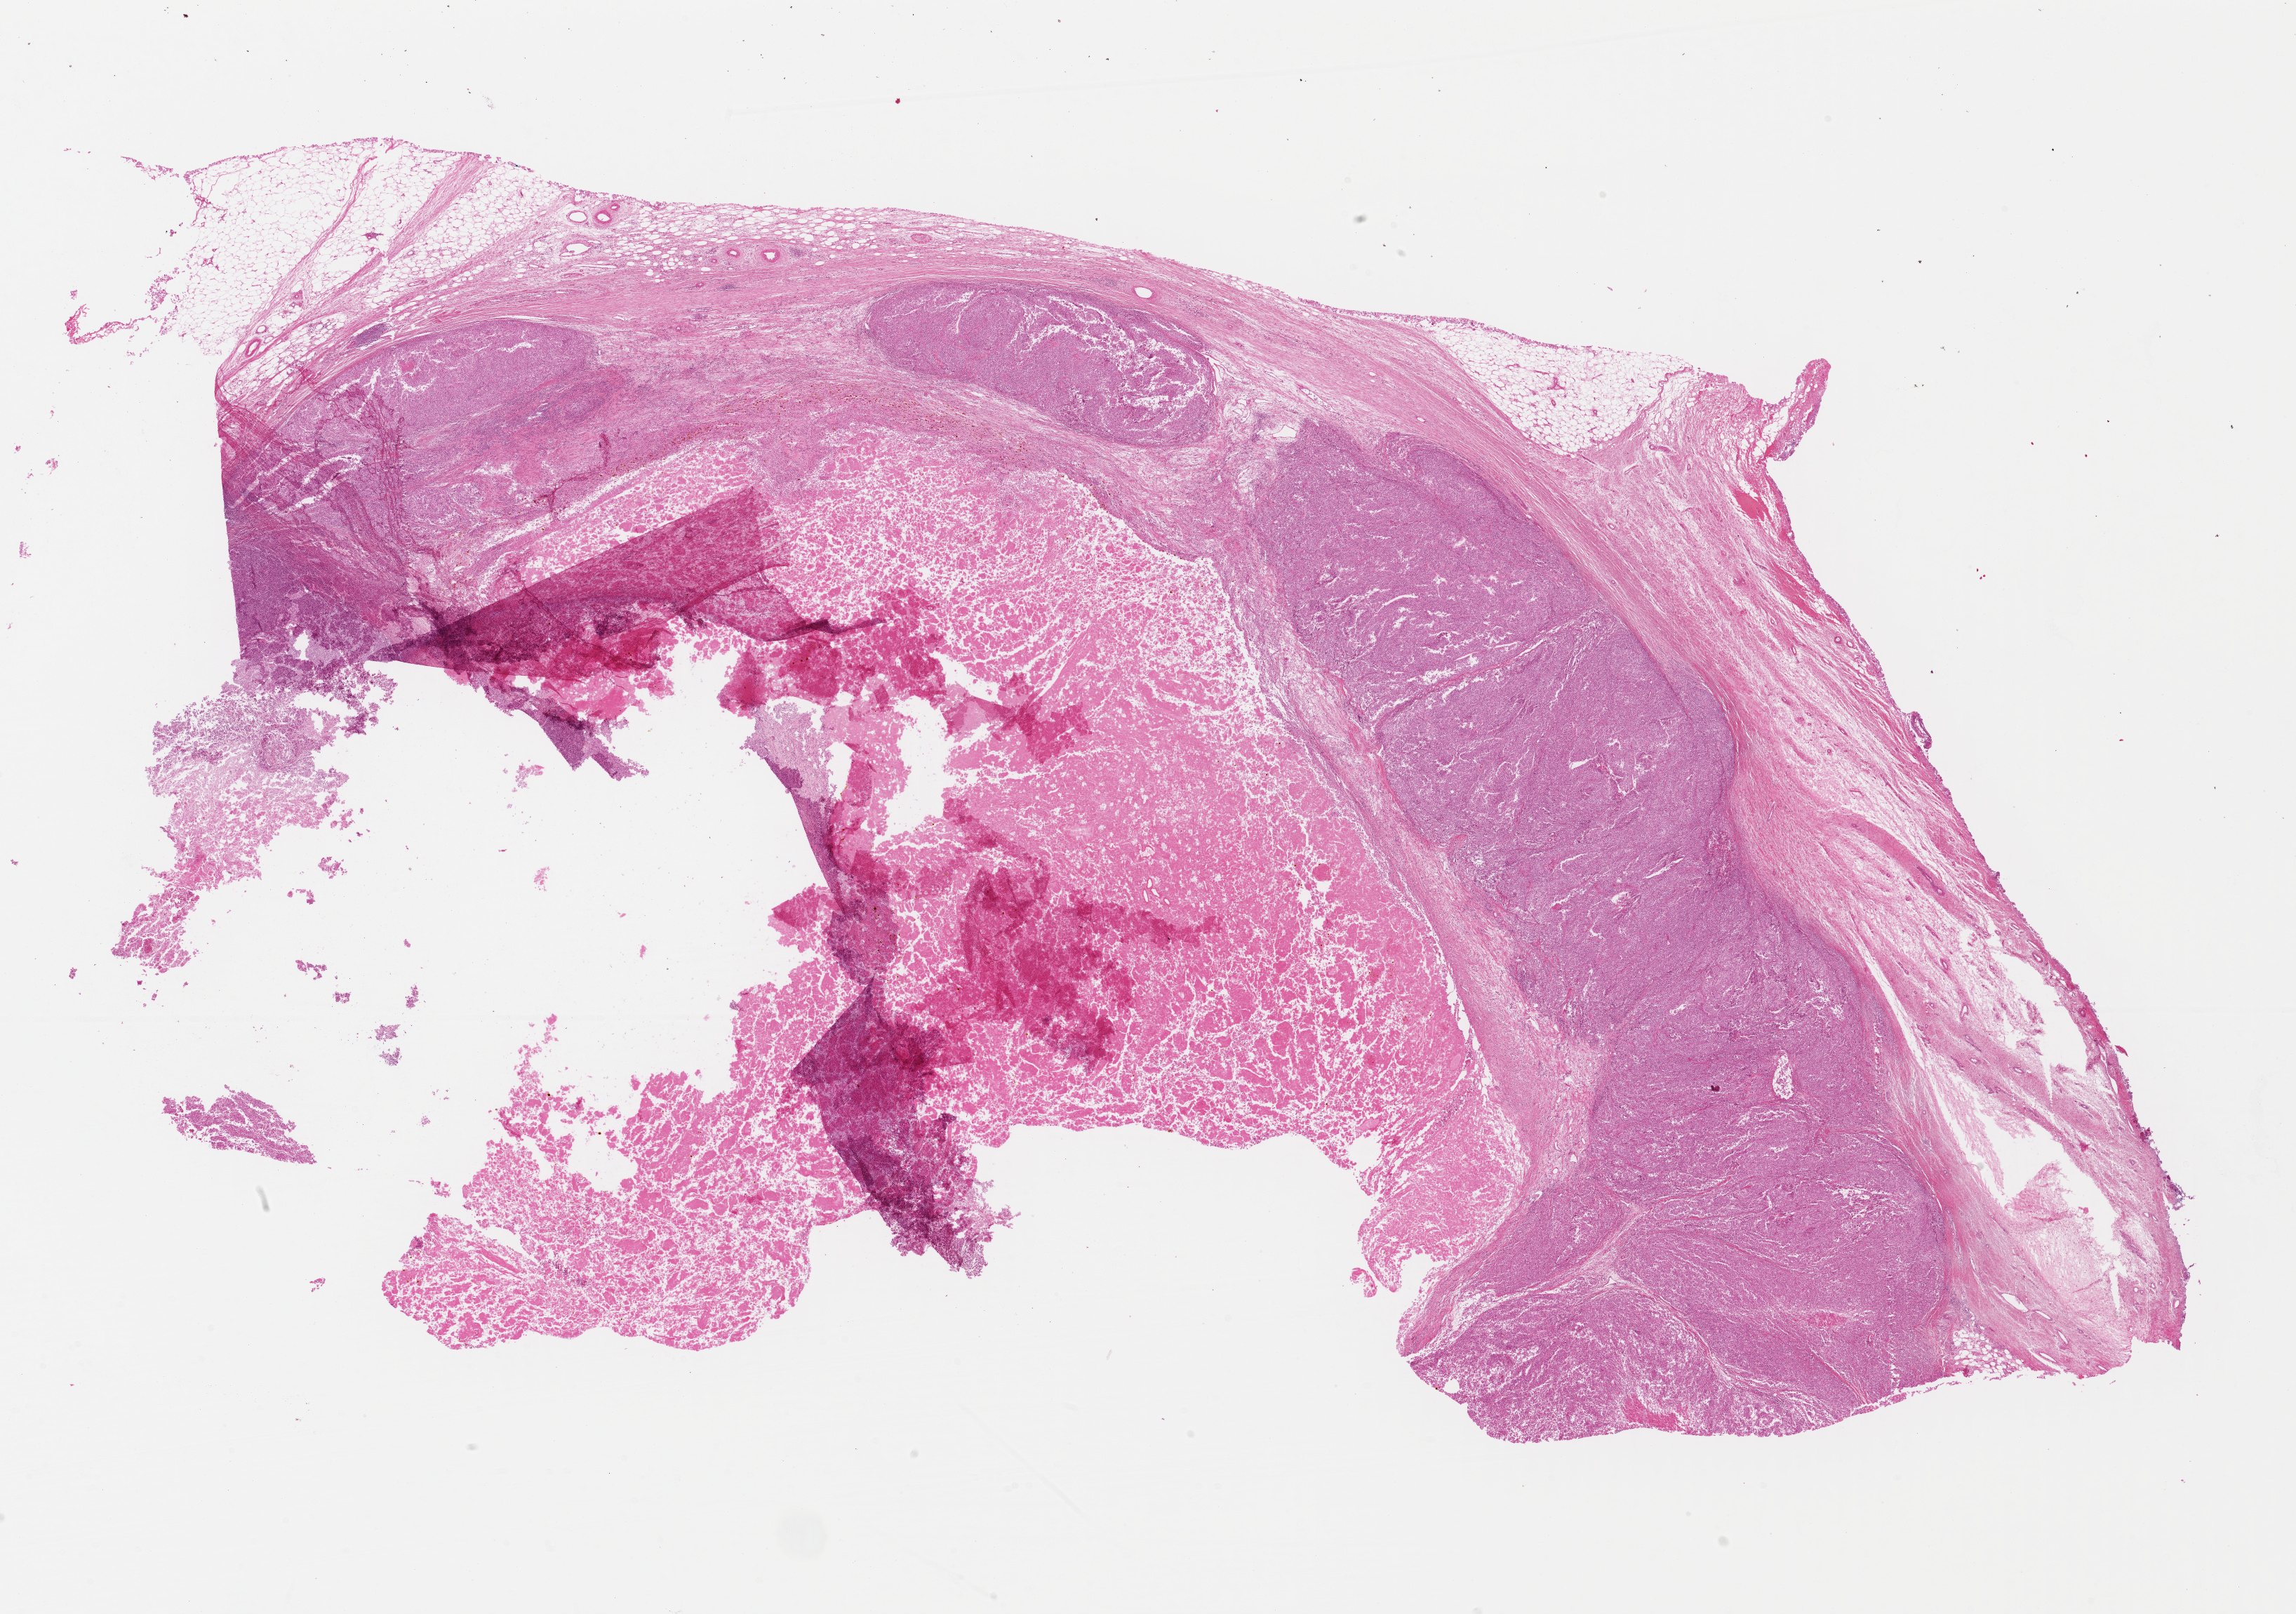
H&E-stained whole-slide image, shown as a low-resolution overview of the whole scanned area (about 25.7 x 18.1 mm), formalin-fixed paraffin-embedded (FFPE) diagnostic section, primary tumour sample from the skin. Male patient; age at initial diagnosis 52 years.
• pathologic diagnosis: Malignant melanoma, NOS